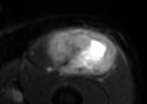
MRI of an extremity soft-tissue mass, one axial slice. Slice 48 of 85 in the series (ordered by position). T2-weighted fat-saturated. MR volume resampled by the dataset authors to the PET/CT grid (not the native acquisition matrix). 3.27 mm slice thickness. 147 × 104 image matrix, field of view 144 × 102 mm. Male patient. Case-level facts recorded for this patient, not image findings: histological type: extraskeletal osteosarcoma; grade: high; site of the primary tumour: thigh.
Outlined on this slice (expert contour drawn on MRI and transferred to this co-registered scan by the dataset authors):
- gross tumour volume (mass): box from (x=46, y=28) to (x=116, y=75) px